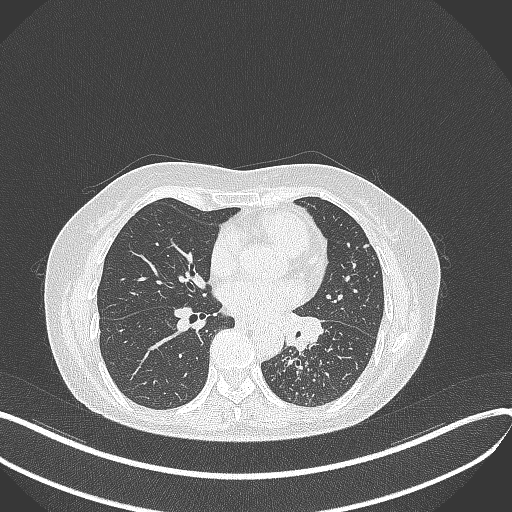
Chest CT, one axial slice; position 194 of 429 along the scan axis; reconstruction kernel B70f; lung window (W 1500 / L -600 HU); 1 mm slice thickness; 512 × 512 image matrix. Patient: female, 63 years. From the clinical record (not read from this slice): clinical TNM (as recorded): T1b N0 M0.
Outlined on this slice (rectangle marked by the reading radiologist):
- lung tumour (recorded histology: adenocarcinoma): bounding box (x1, y1, x2, y2) in pixels: (282, 305, 334, 357)